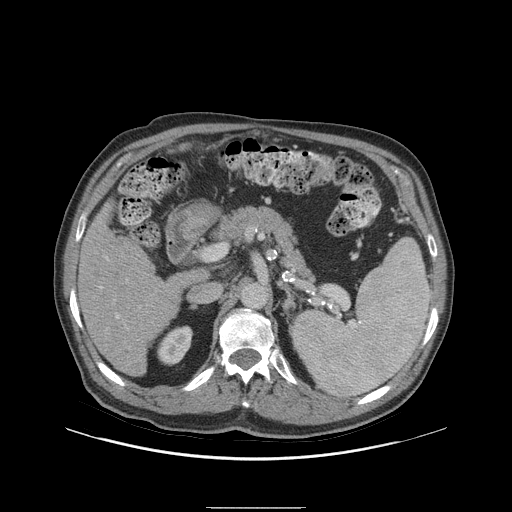
Contrast-enhanced abdominal CT (liver protocol), one axial slice. Slice 48 of 105 in the series (ordered by position). Reconstruction kernel STANDARD. Soft-tissue window (W 400 / L 40 HU). 512 × 512 image matrix, field of view 440 × 440 mm. Case-level facts recorded for this patient, not image findings: diagnosis: hepatocellular carcinoma (patient treated with transarterial chemoembolisation; whether this scan precedes or follows treatment is not stated here); TNM stage (as recorded): Stage-I; Child-Pugh class: A; tumour size: 5.1 cm.
Structures marked on this image (semi-automatically segmented with operator editing):
- liver parenchyma outside the tumour (the mass and vessels are separate outlines, so this box may not span the whole liver): bounding box (x1, y1, x2, y2) in pixels: (78, 204, 198, 376)
- liver vessels: (100, 258, 119, 318)